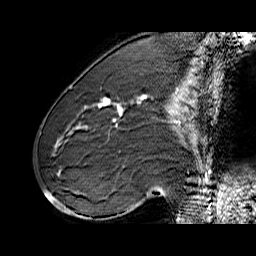
Breast MRI (dynamic contrast-enhanced), one sagittal slice; slice 25 of 60 in the series (ordered by position); dynamic contrast-enhanced series, time point 2 of 6 at this slice position (early post-contrast); 1.5 T; TE 6.4 ms, TR 32.9 ms; 4 mm slice thickness; 256 × 256 image matrix. Female patient. Case-level facts recorded for this patient, not image findings: setting: breast cancer imaged before/during neoadjuvant chemotherapy; receptor status: HER2-positive.
Outlined on this slice (semi-automatic segmentation, software-assisted and operator-edited):
- analysis volume of interest (the breast-tissue region the enhancement analysis was run in; not a lesion): bounding box [x1, y1, x2, y2] px = [71, 80, 155, 146]
- tumour enhancement mask (voxels above the 100 % enhancement threshold inside the analysis volume of interest): [100, 96, 143, 114]